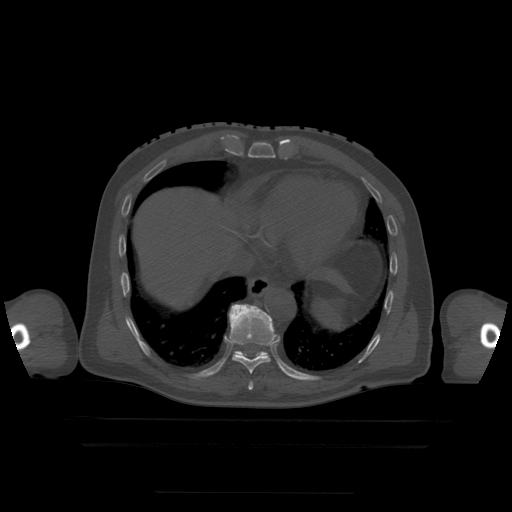
CT including the spine, one axial slice. Slice 257 of 522 in the series (ordered by position). Bone window (W 1800 / L 400 HU). 1.25 mm slice thickness. 512 × 512 image matrix, field of view 436 × 436 mm. Patient age 68 years. Case-level facts recorded for this patient, not image findings: primary cancer: urothelial.
Outlined on this slice (semi-automatic segmentation, software-assisted and operator-edited):
- T10 vertebra: bounding box <233,351,269,357> (left, top, right, bottom; pixels)
- T8 vertebra: <249,382,254,390>
- T9 vertebra: <229,305,277,374>